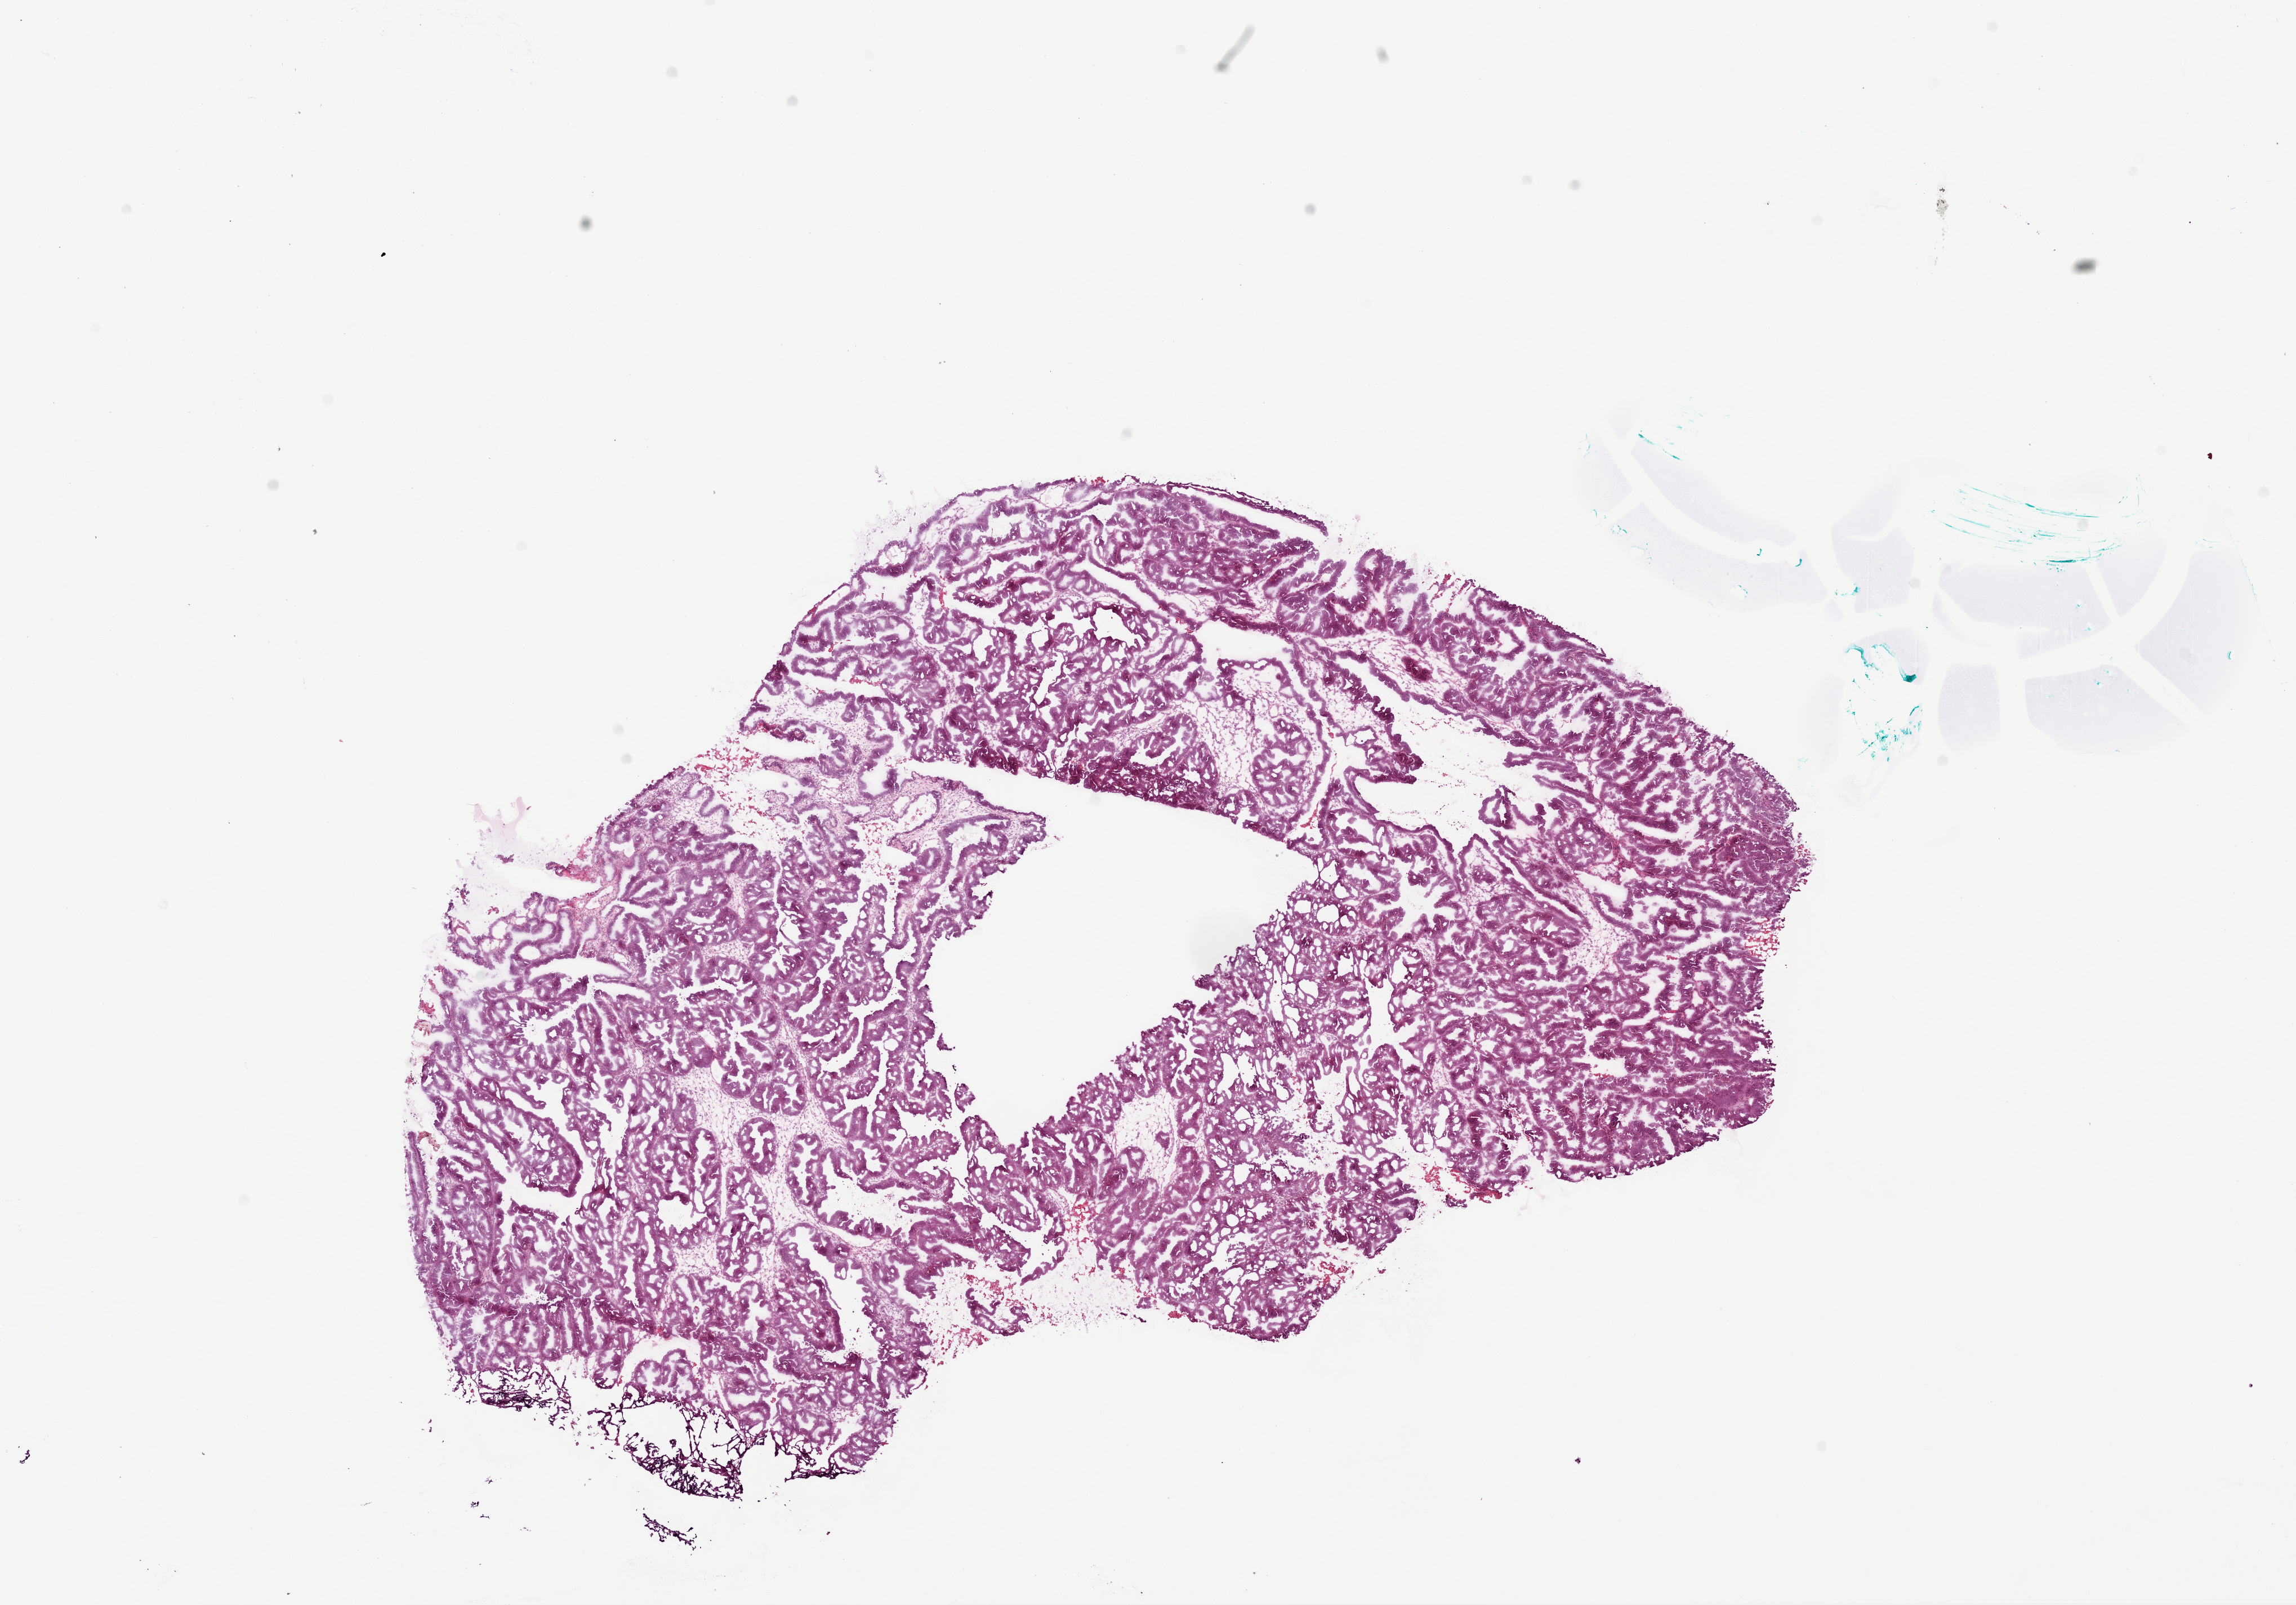
Hematoxylin and eosin (H&E) stained whole-slide image, low-resolution overview of the scanned area, about 16.4 x 11.5 mm (acquisition: 20x scan); frozen section; sample: primary tumour, ovary. Female patient; age at initial diagnosis 50 years. Histologic grade: G3 (poorly differentiated). Slide review estimates, as recorded: tumour cells 85%, tumour nuclei 85%, normal cells 5%, stromal cells 10%, necrosis 0%.
- FIGO stage: IIIC
- diagnosis: Serous cystadenocarcinoma, NOS